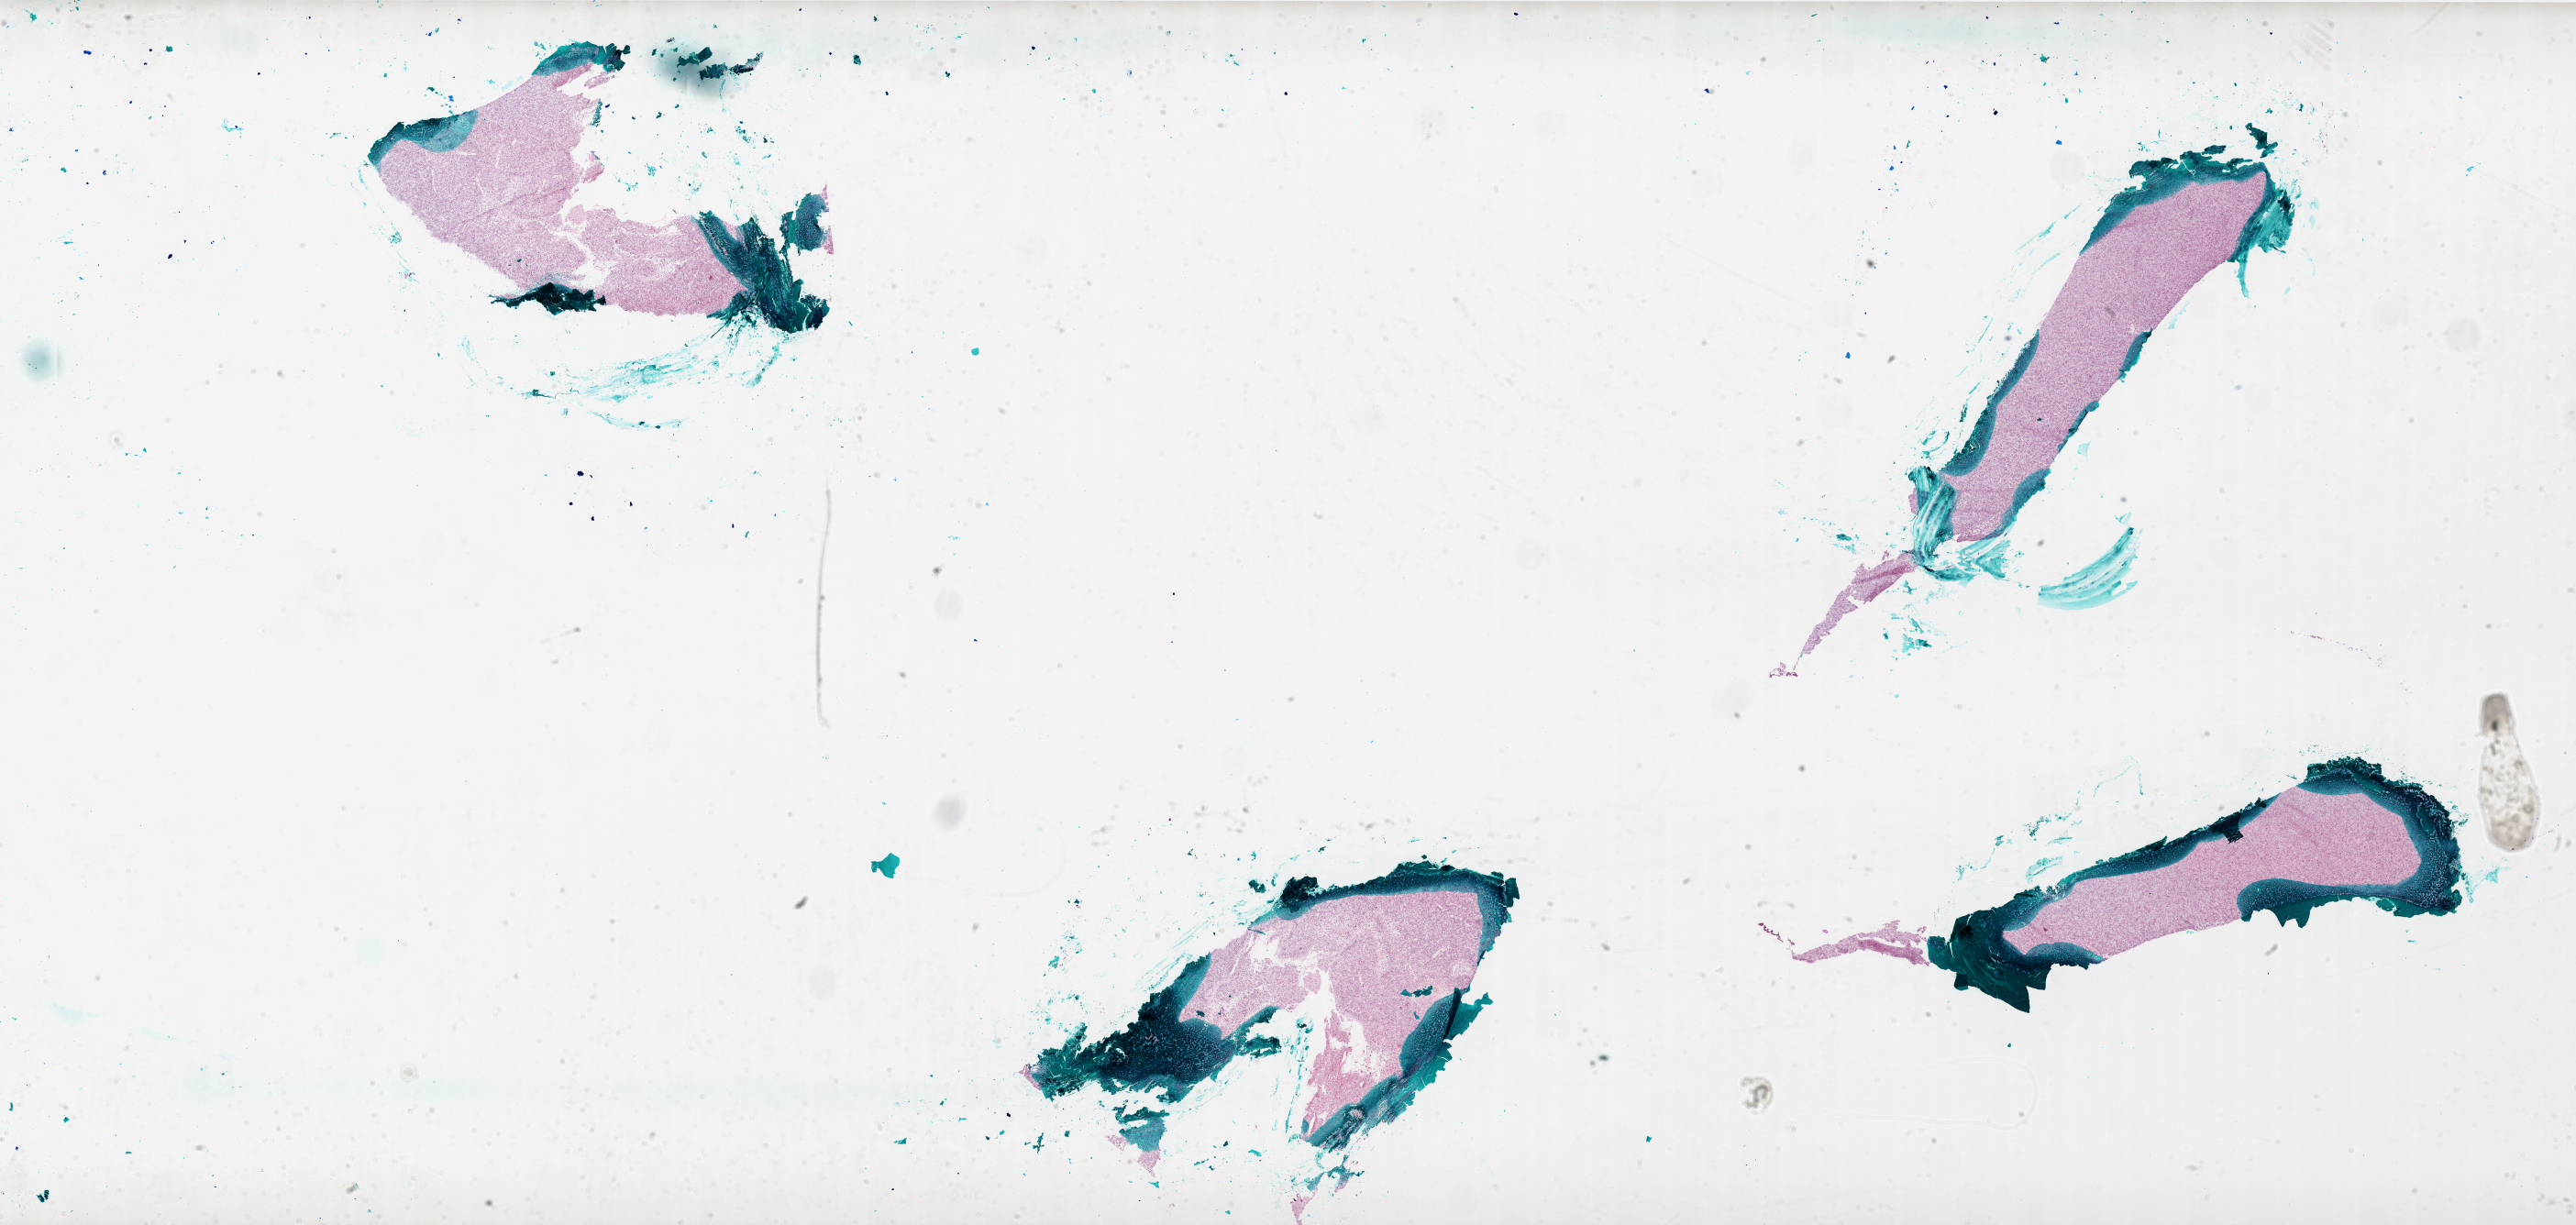
Whole-slide histology image, H&E — low-resolution overview of the scanned area, about 45.0 x 21.4 mm. Frozen section from the bottom of the tissue portion. Brain, primary tumour sample. Patient: male, age at initial diagnosis 50 years. Composition of this section per pathologist review: tumour cells 80%, tumour nuclei 100%, normal cells 0%, stromal cells 0%, necrosis 20%.
Diagnosis: Glioblastoma.